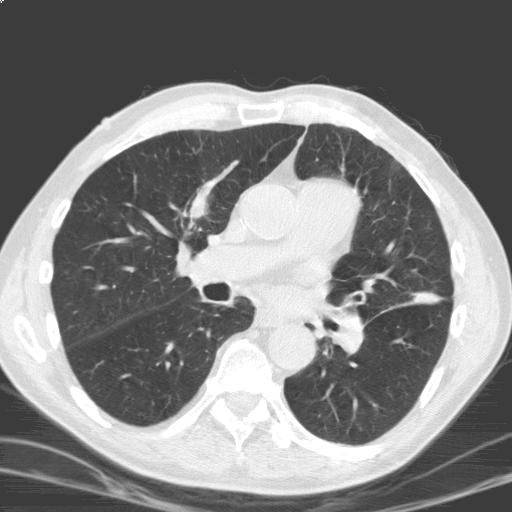
Axial slice from a low-dose chest CT screening exam. Second annual screen. Lung window (W 1500 / L -600 HU). Standard (soft-tissue) reconstruction kernel (C). 120 kVp. Slice 84 of 184 in the series. Male, age 69 years at enrolment. Current smoker at enrolment.
Expert reader's lesion annotation, bounding box <174,177,231,232> (left, top, right, bottom; pixels). The screening reader recorded 2 non-calcified nodules or masses ≥4 mm on this exam; which of them this box marks is not recorded. Lung cancer was diagnosed 17 days after this screen: squamous cell carcinoma, NOS, right upper lobe, moderately differentiated (G2), stage IB (AJCC 6th edition), 40 mm at pathology.